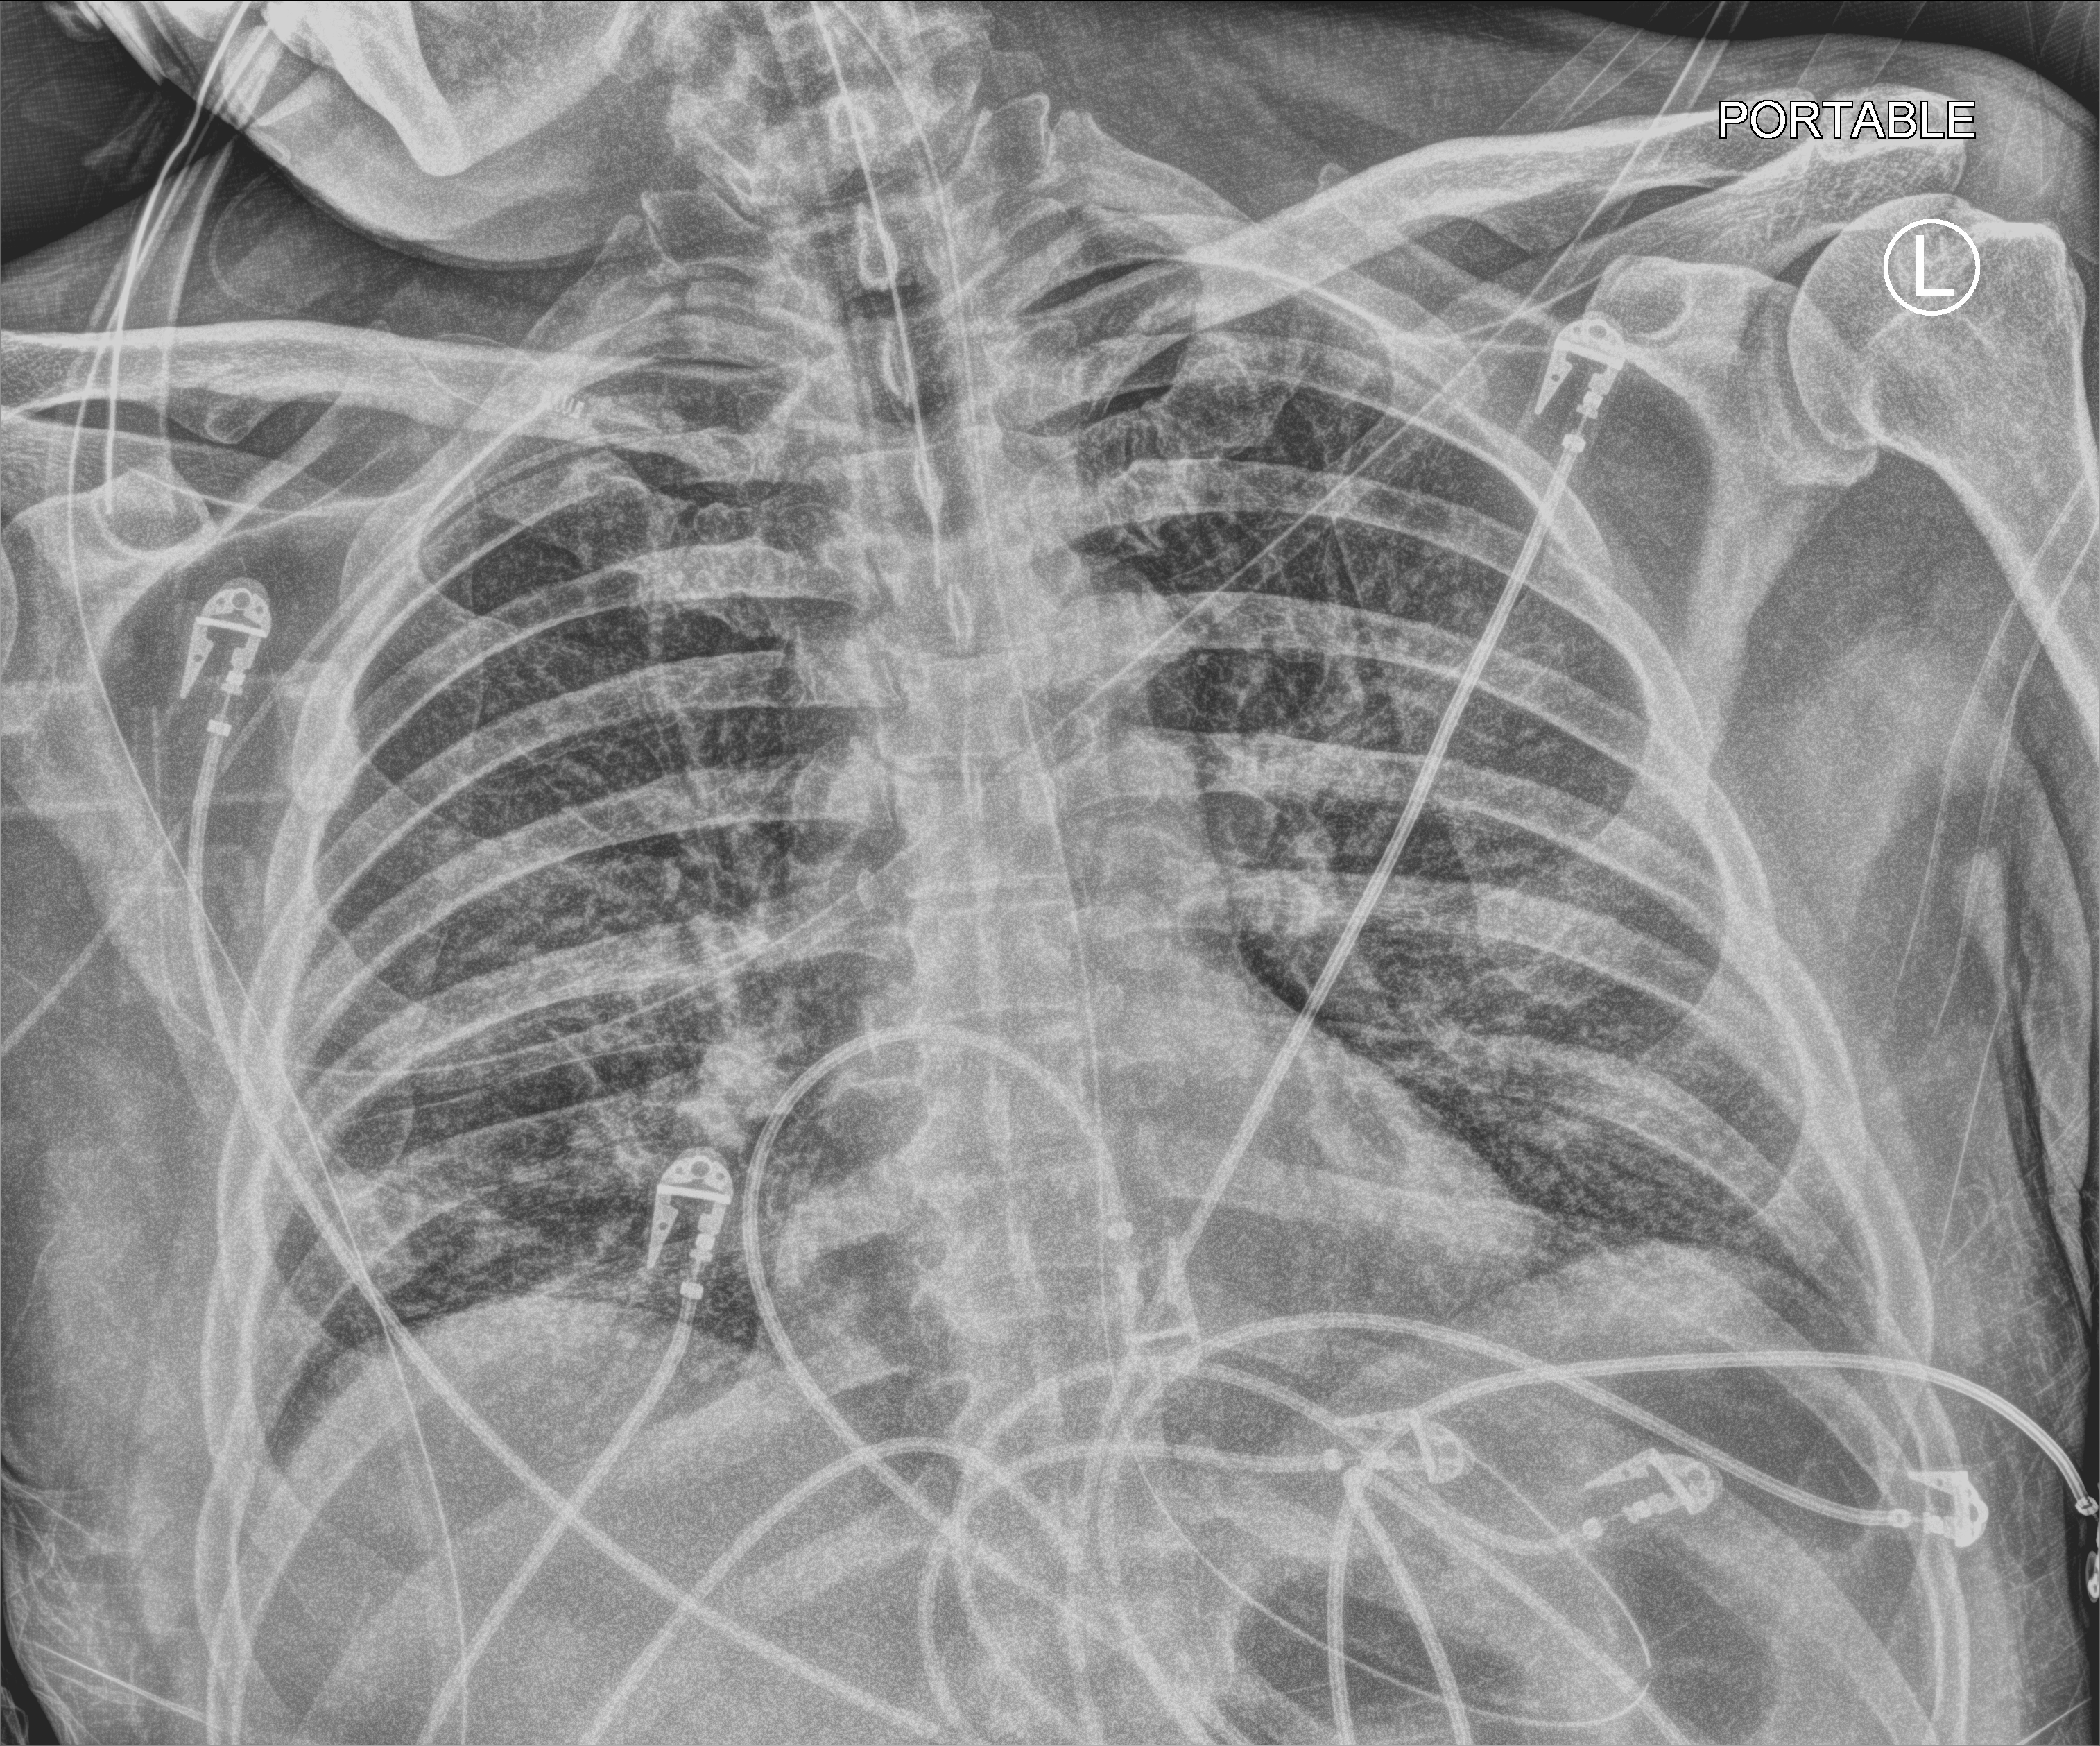
Chest X-ray (portable). Male patient hospitalised with COVID-19, age 60–74 years.
From the hospital-stay record, not from the radiograph (when in the stay this image was taken is not recorded):
- admitted to intensive care during this hospital stay: yes
- hypertension (admission record): no
- other chronic lung disease (admission record): no